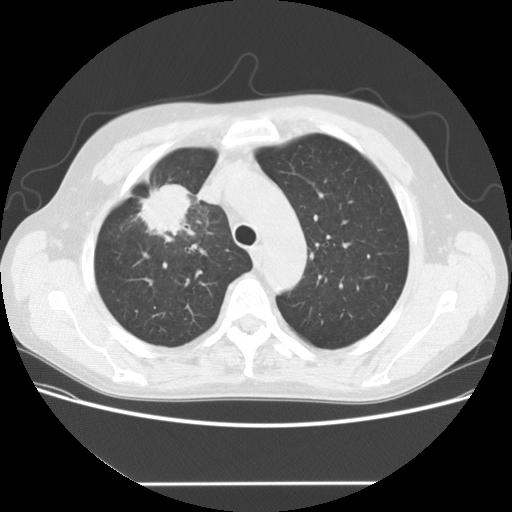
Low-dose screening chest CT, one axial slice; slice 118 of 153 in the series (ordered by position); reconstruction kernel STANDARD; lung window (W 1500 / L -600 HU); 2.5 mm slice thickness; 512 × 512 image matrix, field of view 360 × 360 mm.
Annotated regions visible in this slice (expert manual segmentation):
- lesion 1 (tumor, upper lobe of right lung): box from (x=137, y=184) to (x=192, y=242) px